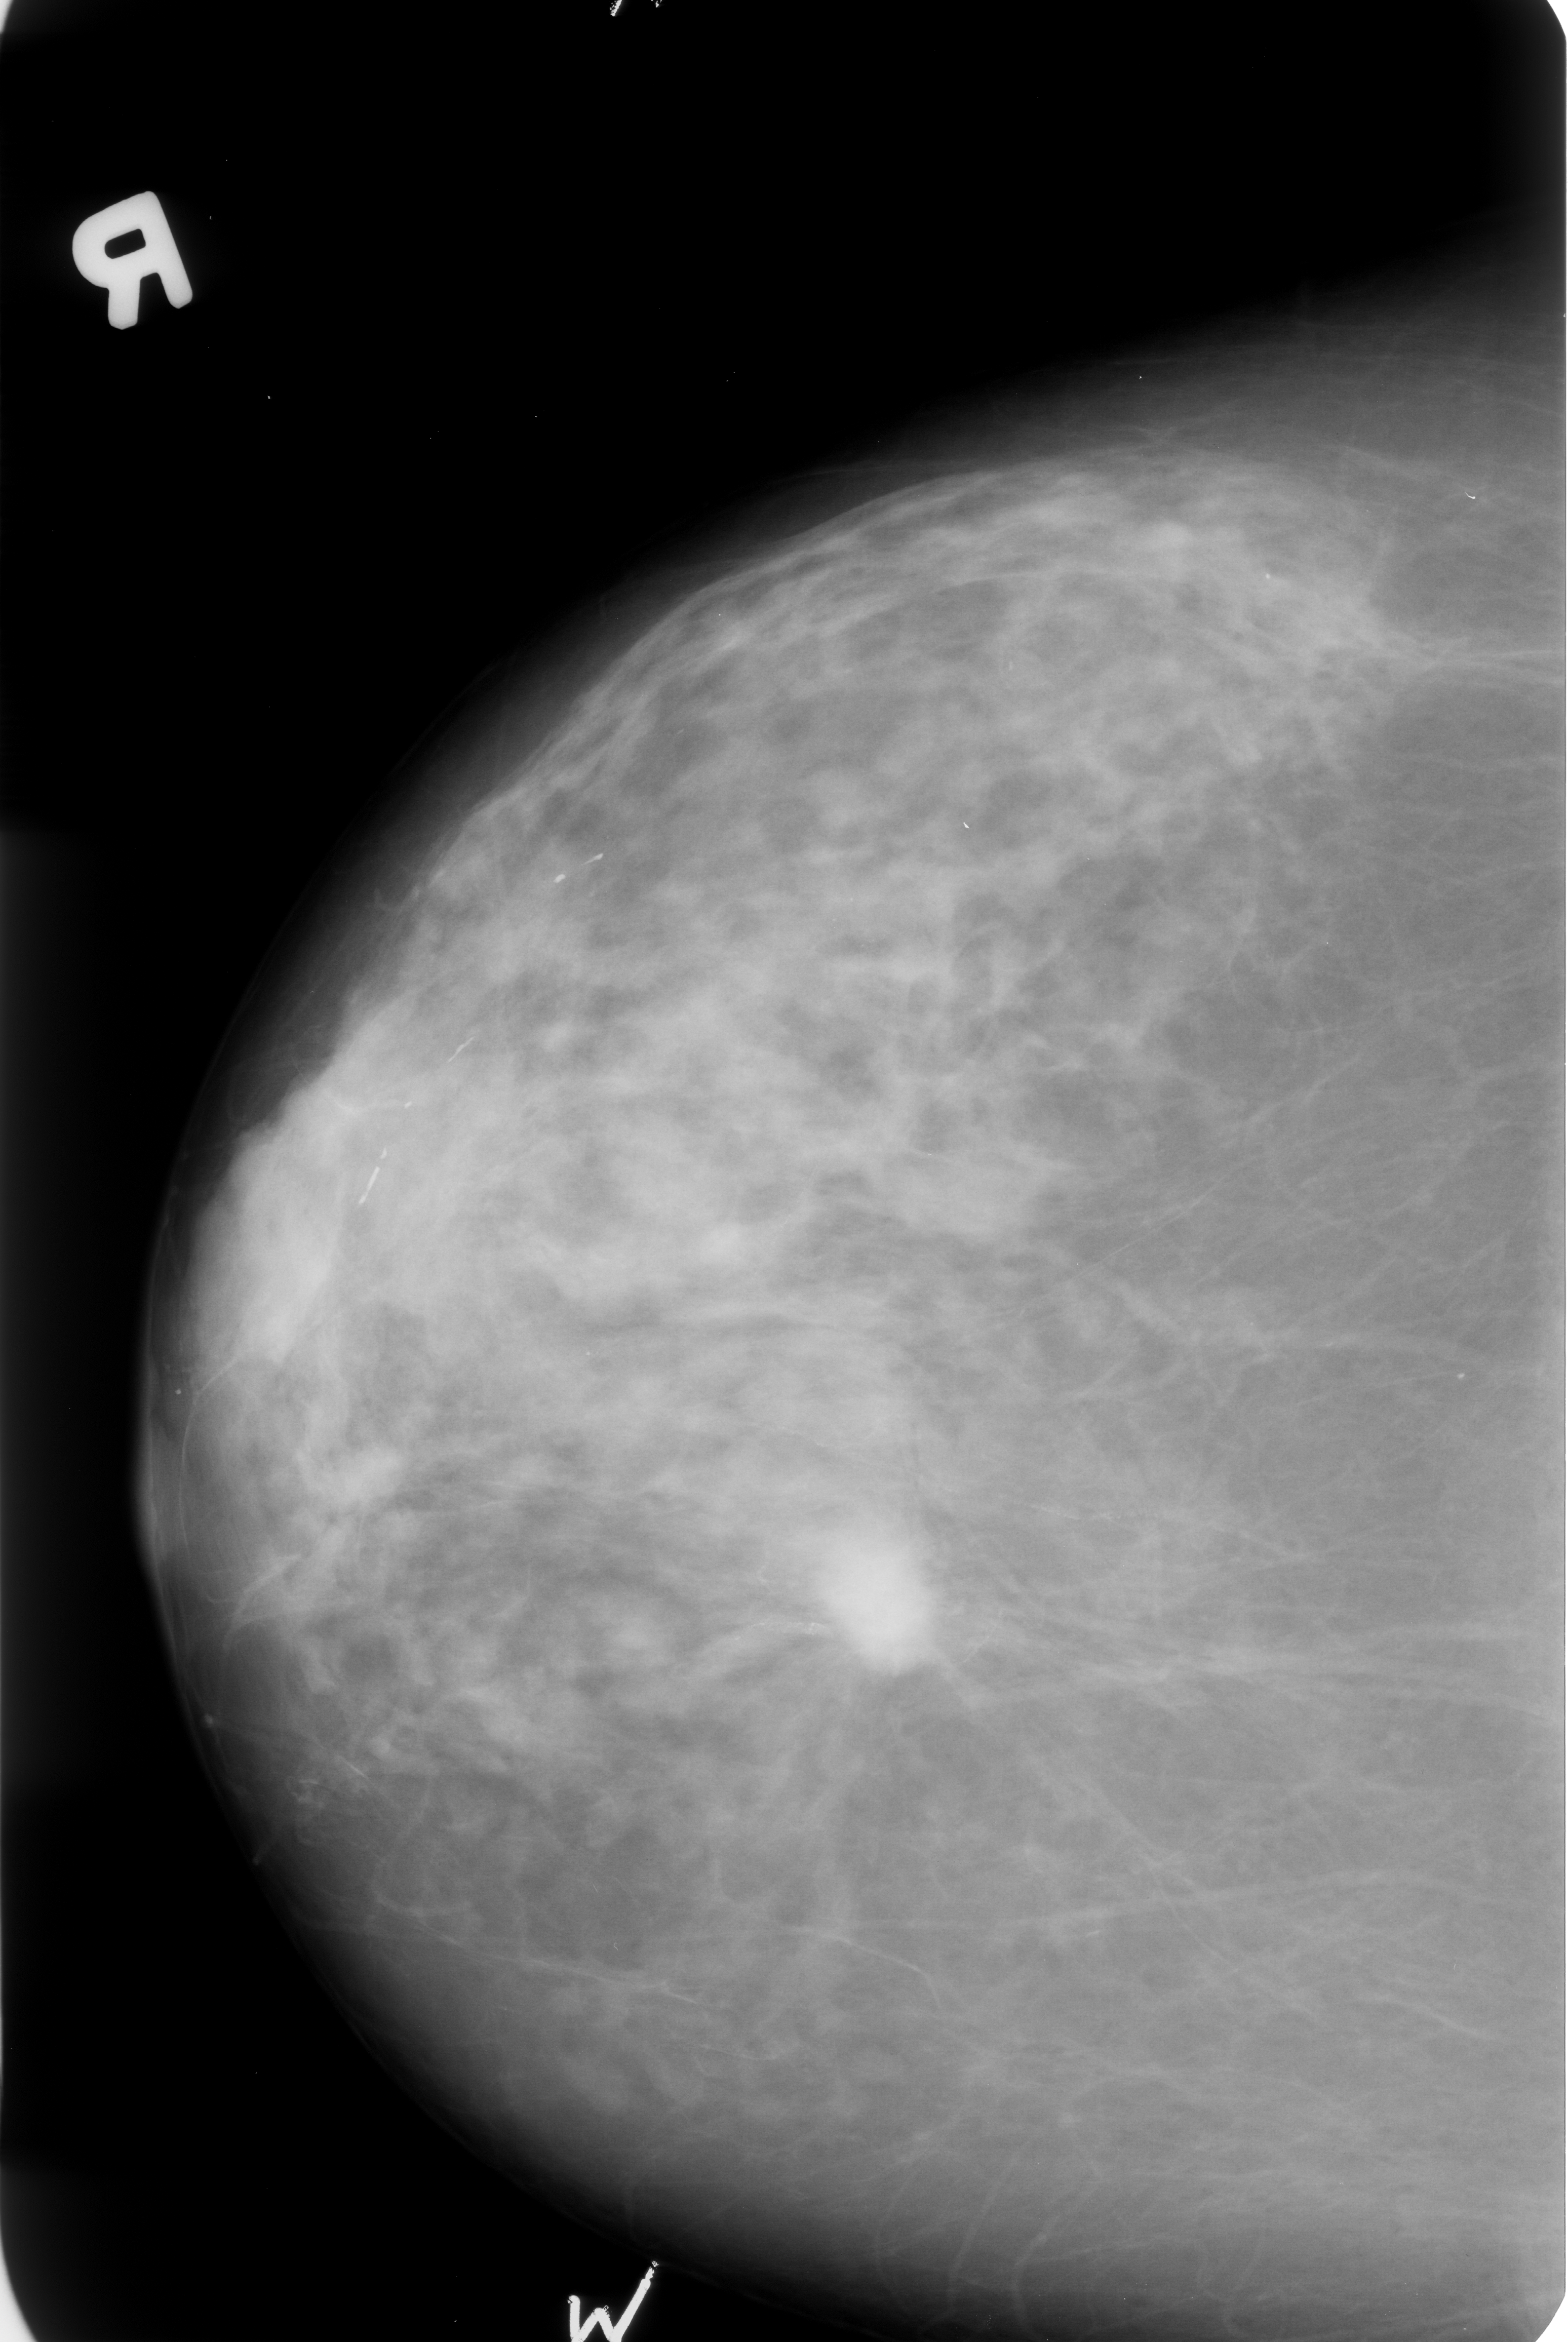
Digitized screen-film mammogram; right breast; CC view; breast composition: heterogeneously dense (BI-RADS density category 3 of 4).
Marked abnormality: mass, shape irregular / architectural distortion, margins spiculated; BI-RADS assessment category 5; pathology result (as recorded, not read from the image): malignant.